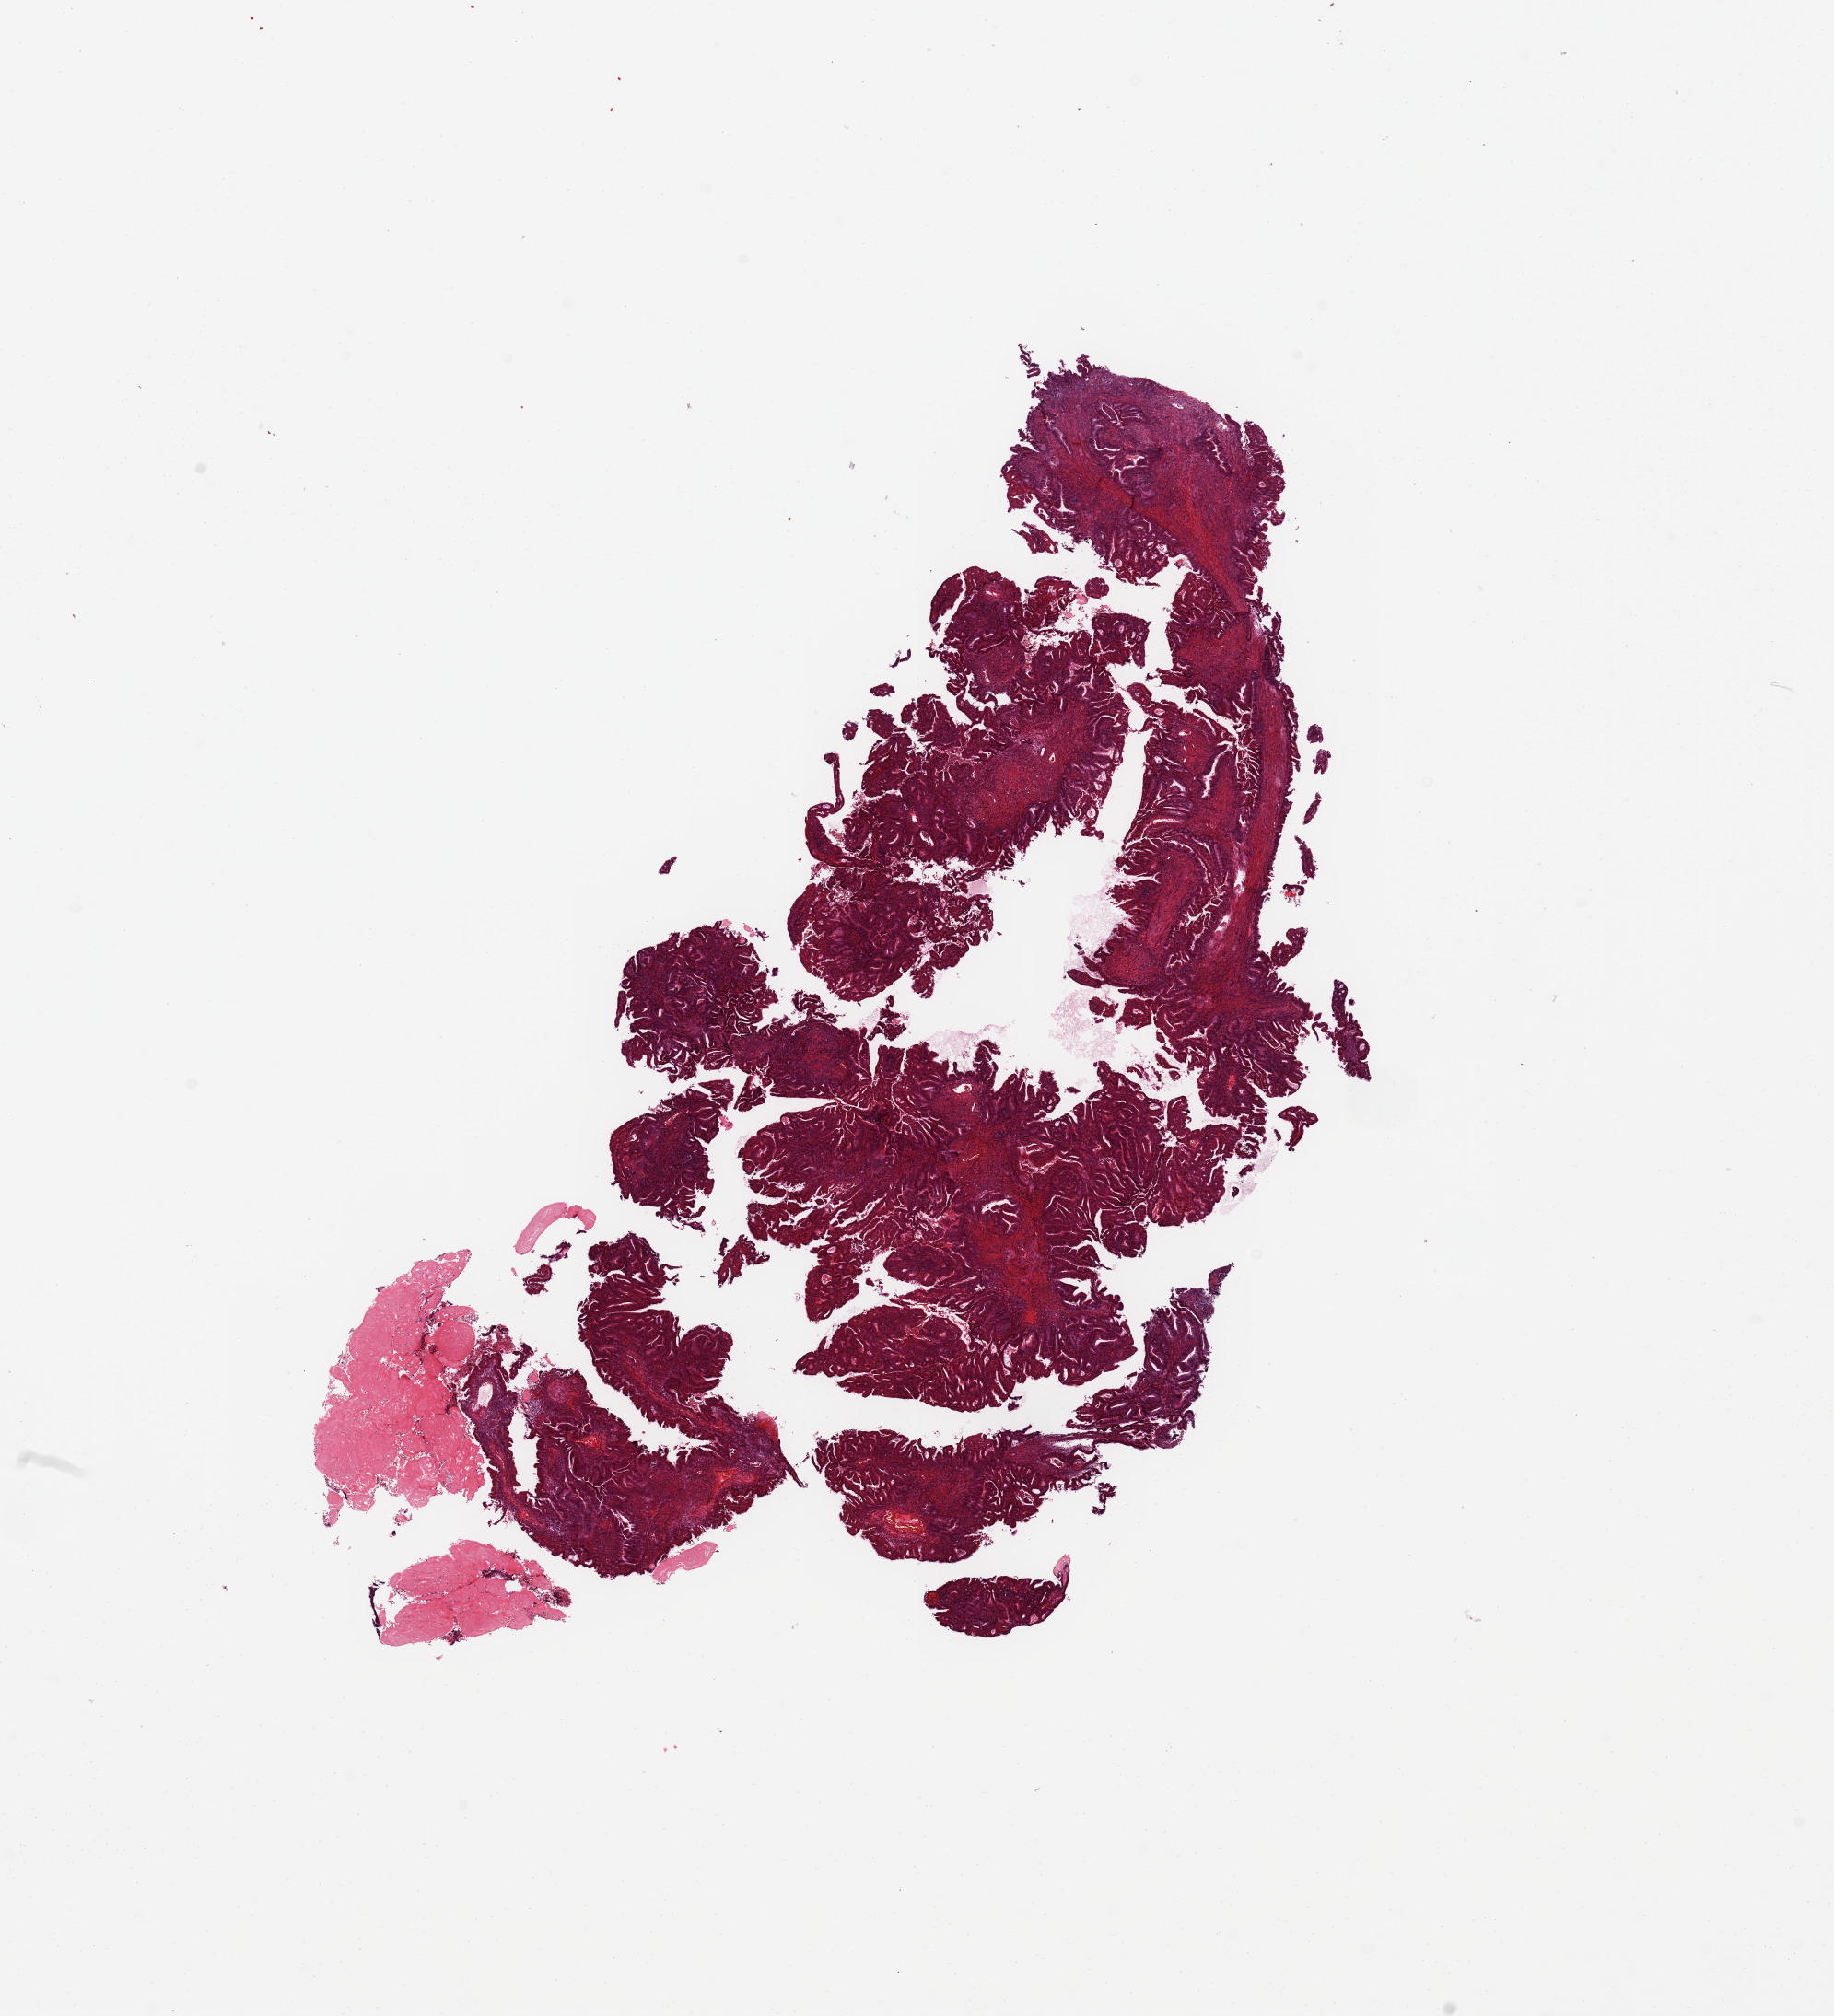
H&E-stained whole-slide image — low-resolution overview of the scanned area, about 15.8 x 17.3 mm, tumour tissue sample, uterus. Patient: female, age 68 years. Histologic grade: G1 (well differentiated).
• AJCC pathologic stage: IIIC1
• diagnosis: Endometrioid adenocarcinoma, NOS